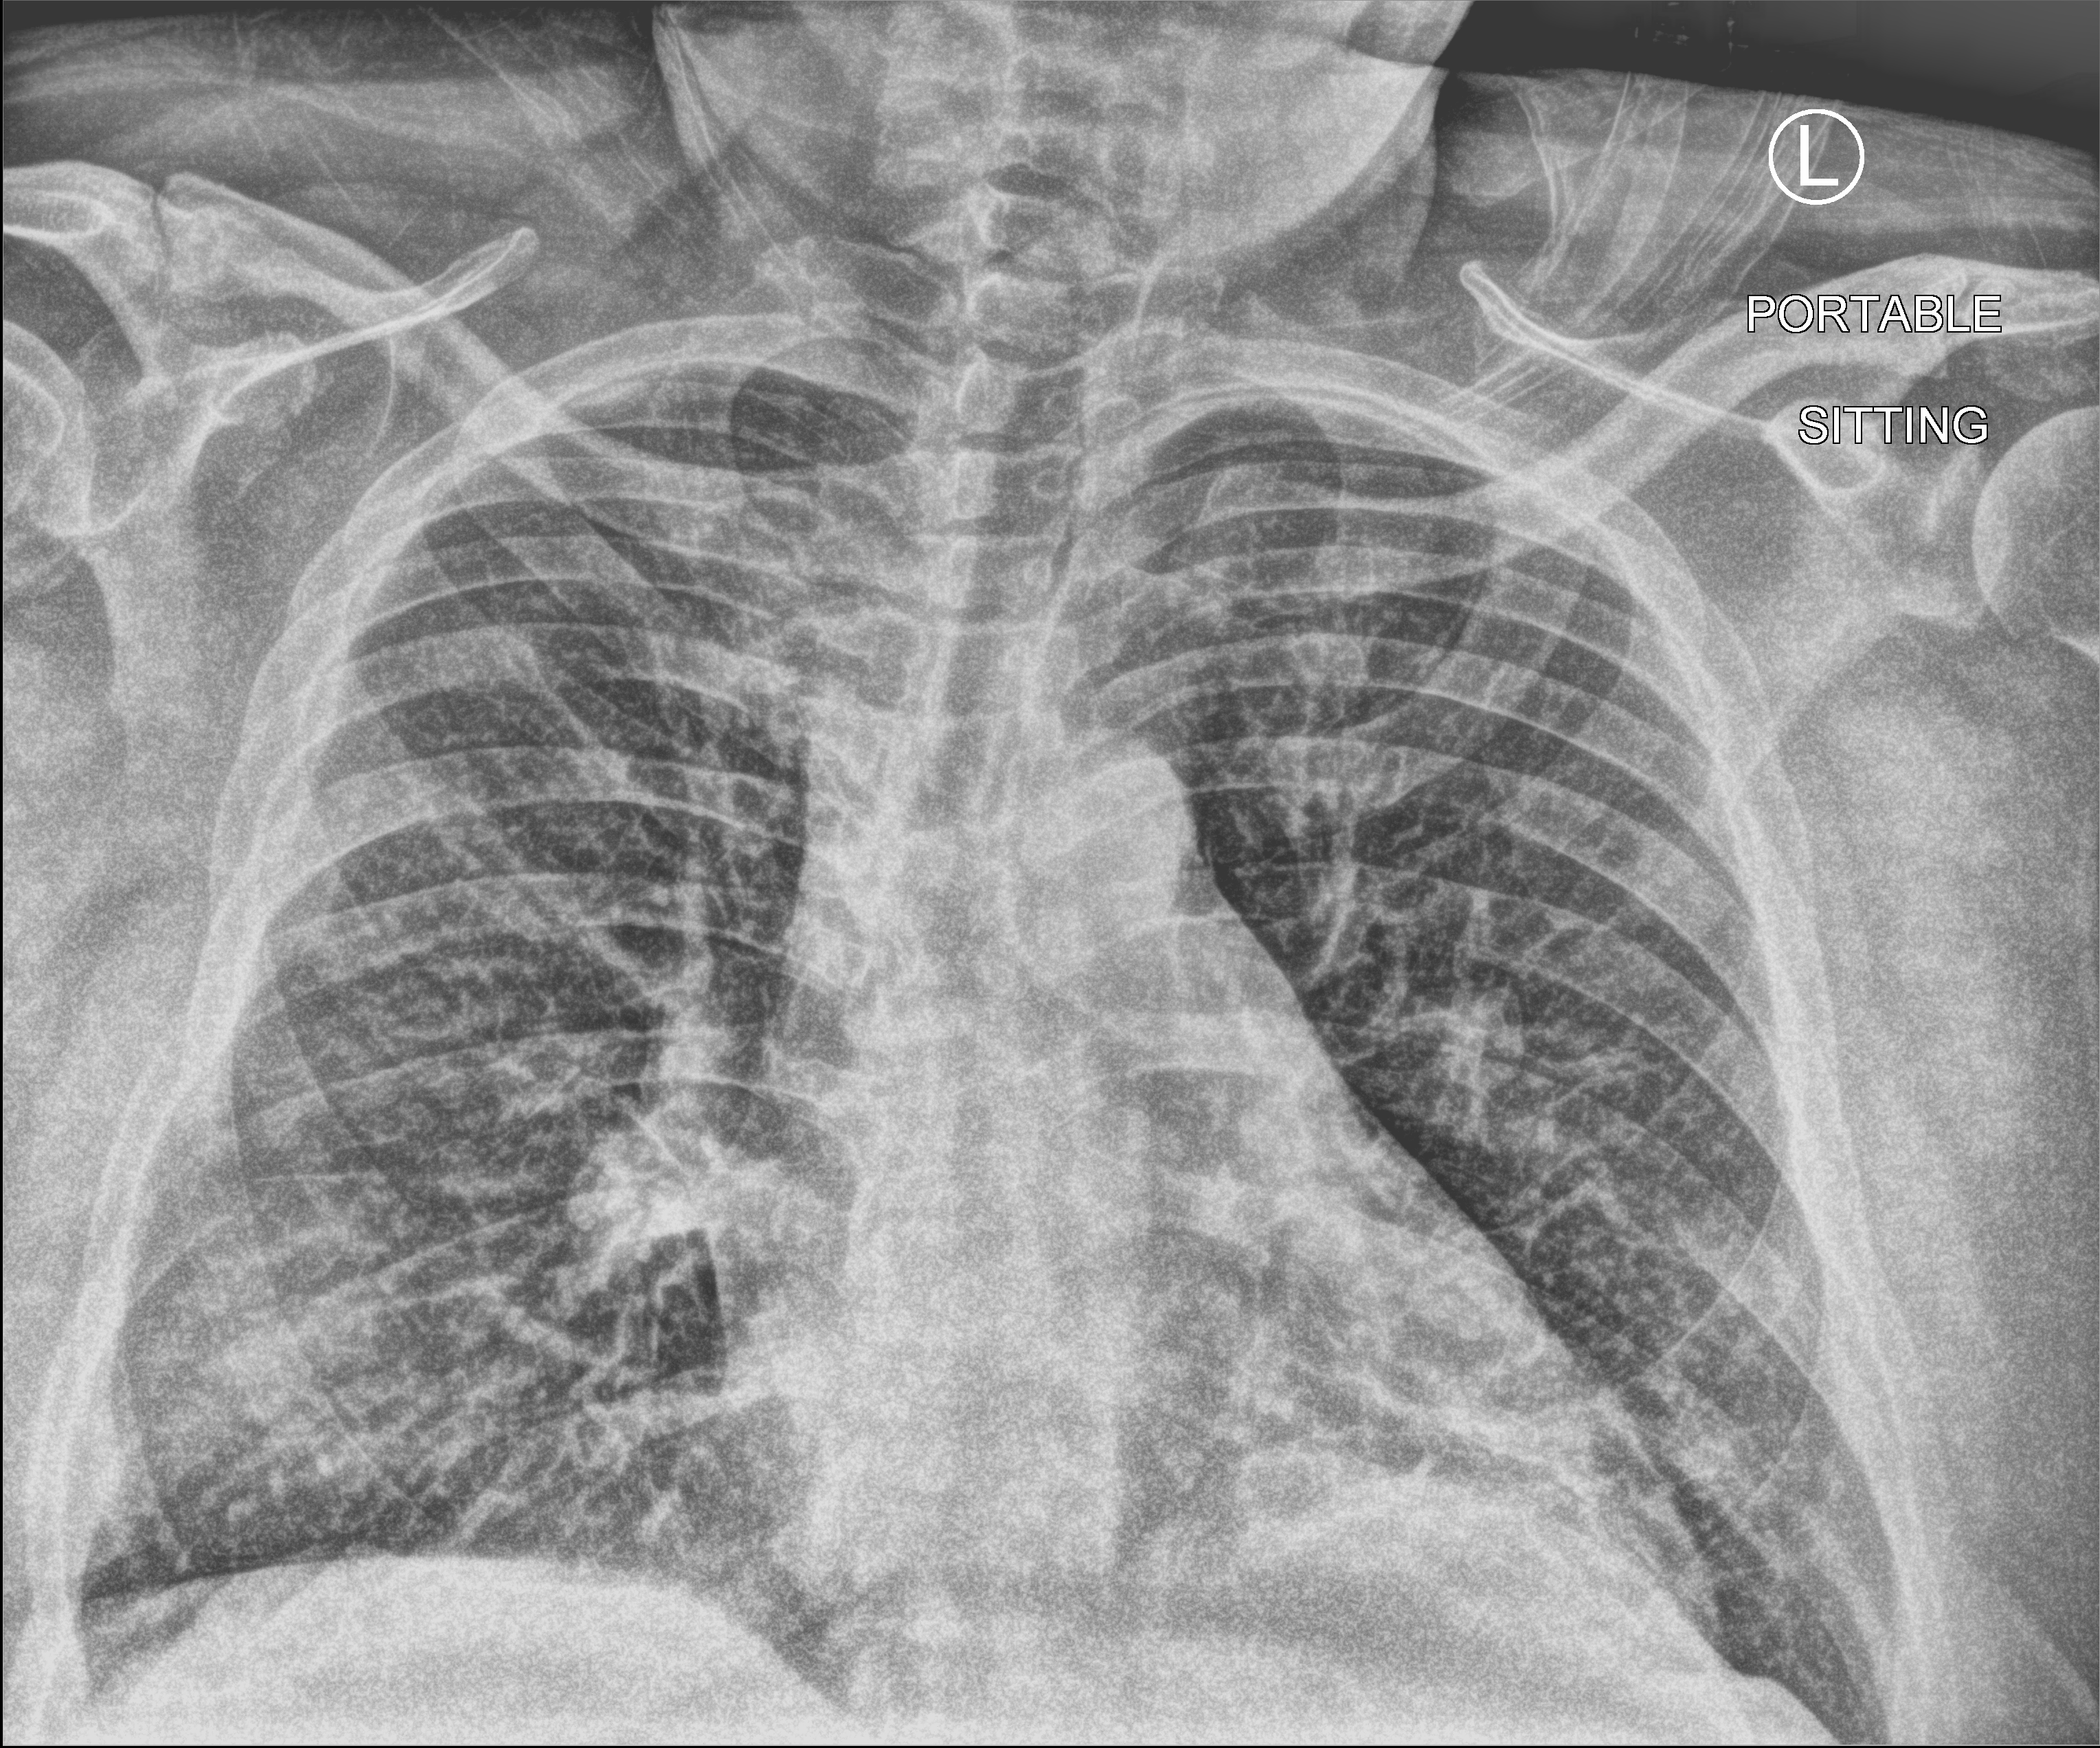
Bedside chest radiograph (computed radiography); anteroposterior (AP) projection. Male patient hospitalised with COVID-19, age 60–74 years.
From the hospital-stay record, not from the radiograph (when in the stay this image was taken is not recorded):
- admitted to intensive care during this hospital stay: yes